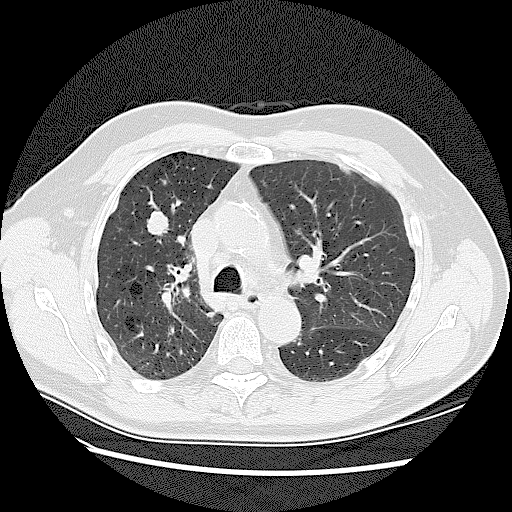
Low-dose screening chest CT, one axial slice. Position 85 of 128 along the scan axis. Reconstruction kernel LUNG. Lung window (W 1500 / L -600 HU). 2.5 mm slice thickness. 512 × 512 image matrix, field of view 360 × 360 mm.
Outlined on this slice (outlined manually by an expert reader):
- lesion 1 (tumor, upper lobe of right lung): bounding box (x1, y1, x2, y2) in pixels: (147, 211, 169, 236)